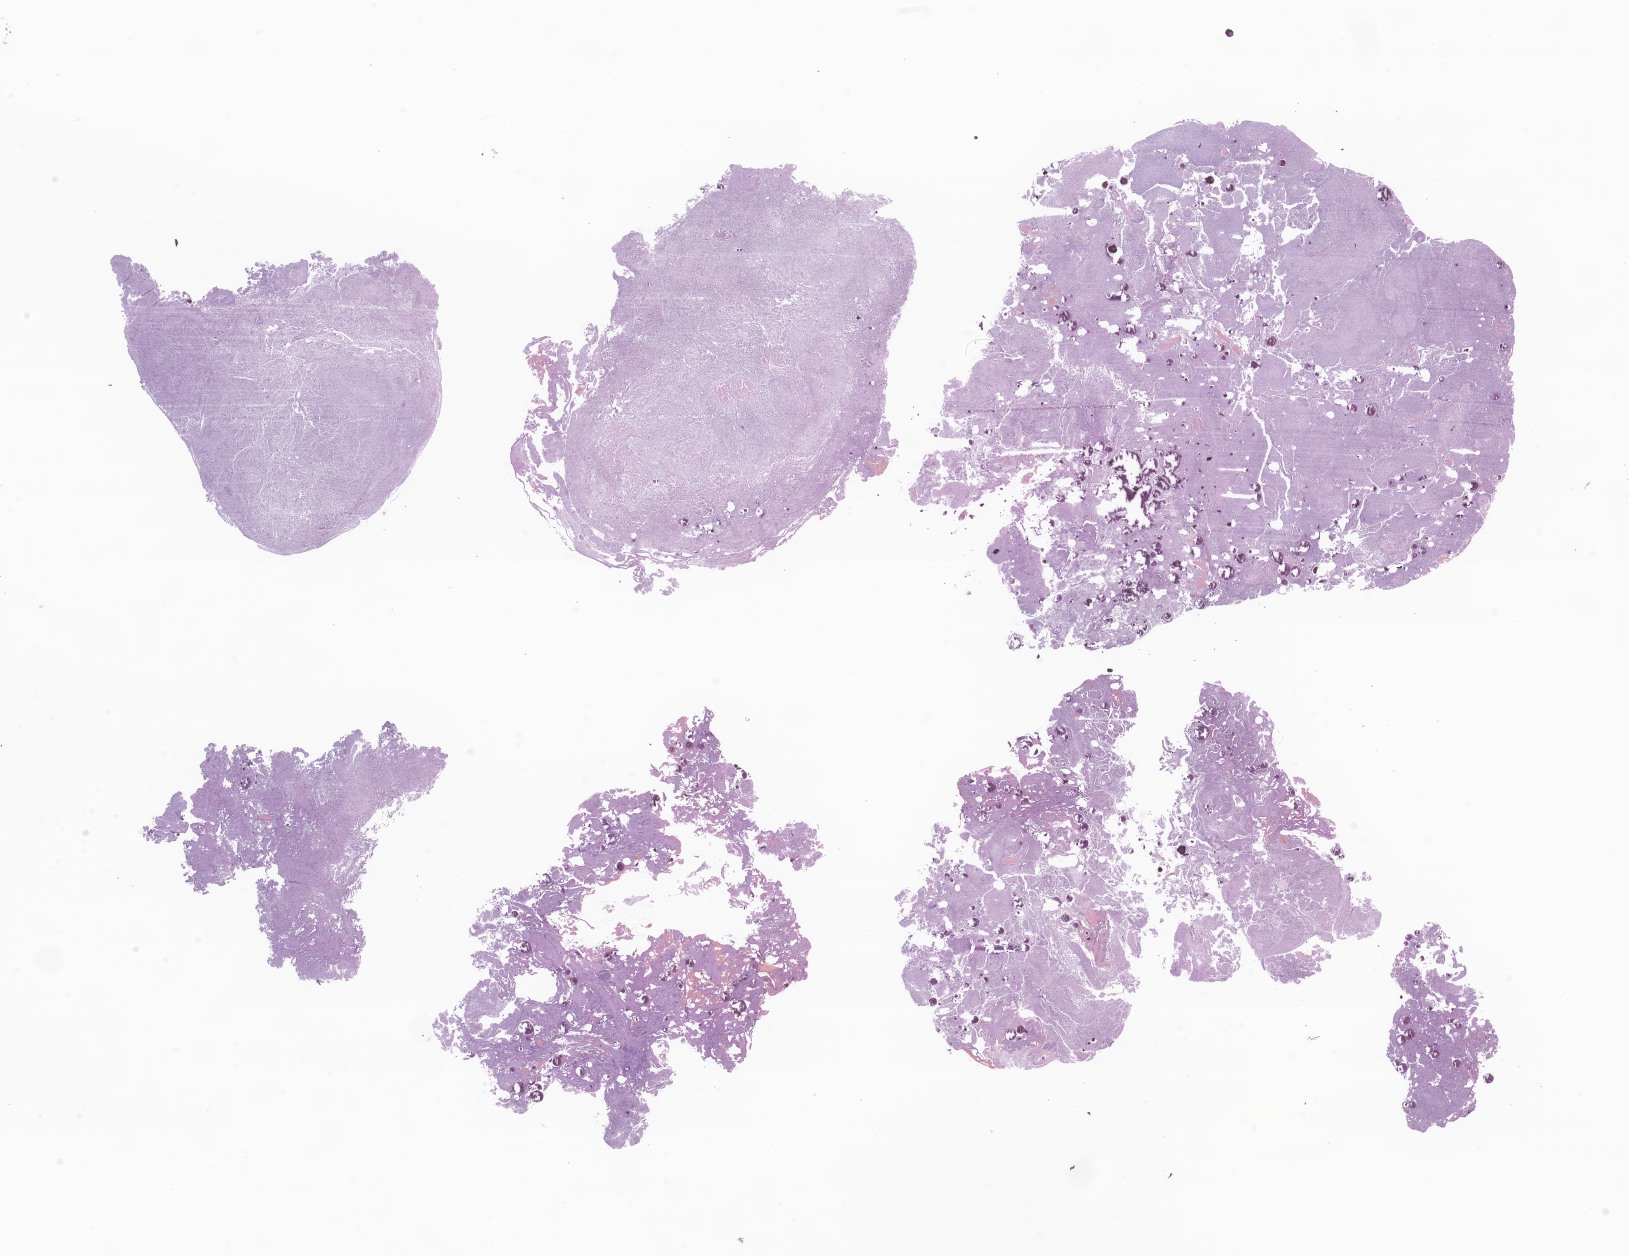
Whole-slide image, haematoxylin and eosin stain of tumor tissue from the cerebellum — low-resolution overview of the scanned area, about 27.5 x 21.2 mm; formalin-fixed, paraffin-embedded (FFPE) tissue. Patient male; age 61 months (5 years 1 month).
Diagnosis: Atypical meningioma.